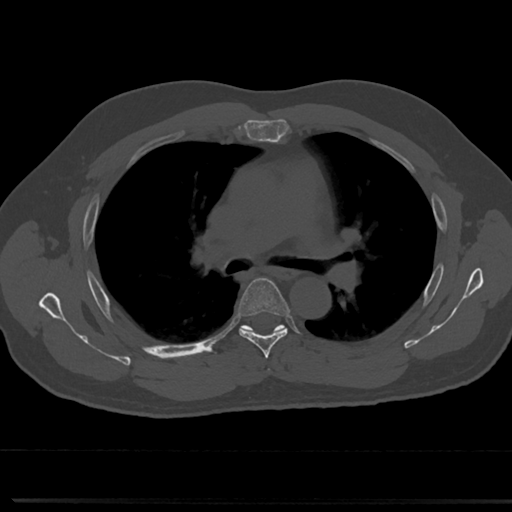
CT including the spine, one axial slice. Position 489 of 817 along the scan axis. 120 kVp. Bone window (W 1800 / L 400 HU). 0.5 mm slice thickness. 512 × 512 image matrix, field of view 355 × 355 mm. Patient: male, 61 years. Case-level facts recorded for this patient, not image findings: primary cancer: prostate.
Outlined on this slice (semi-automatically segmented with operator editing):
- T4 vertebra: bounding box (x1, y1, x2, y2) in pixels: (264, 362, 273, 374)
- T5 vertebra: (226, 278, 295, 349)